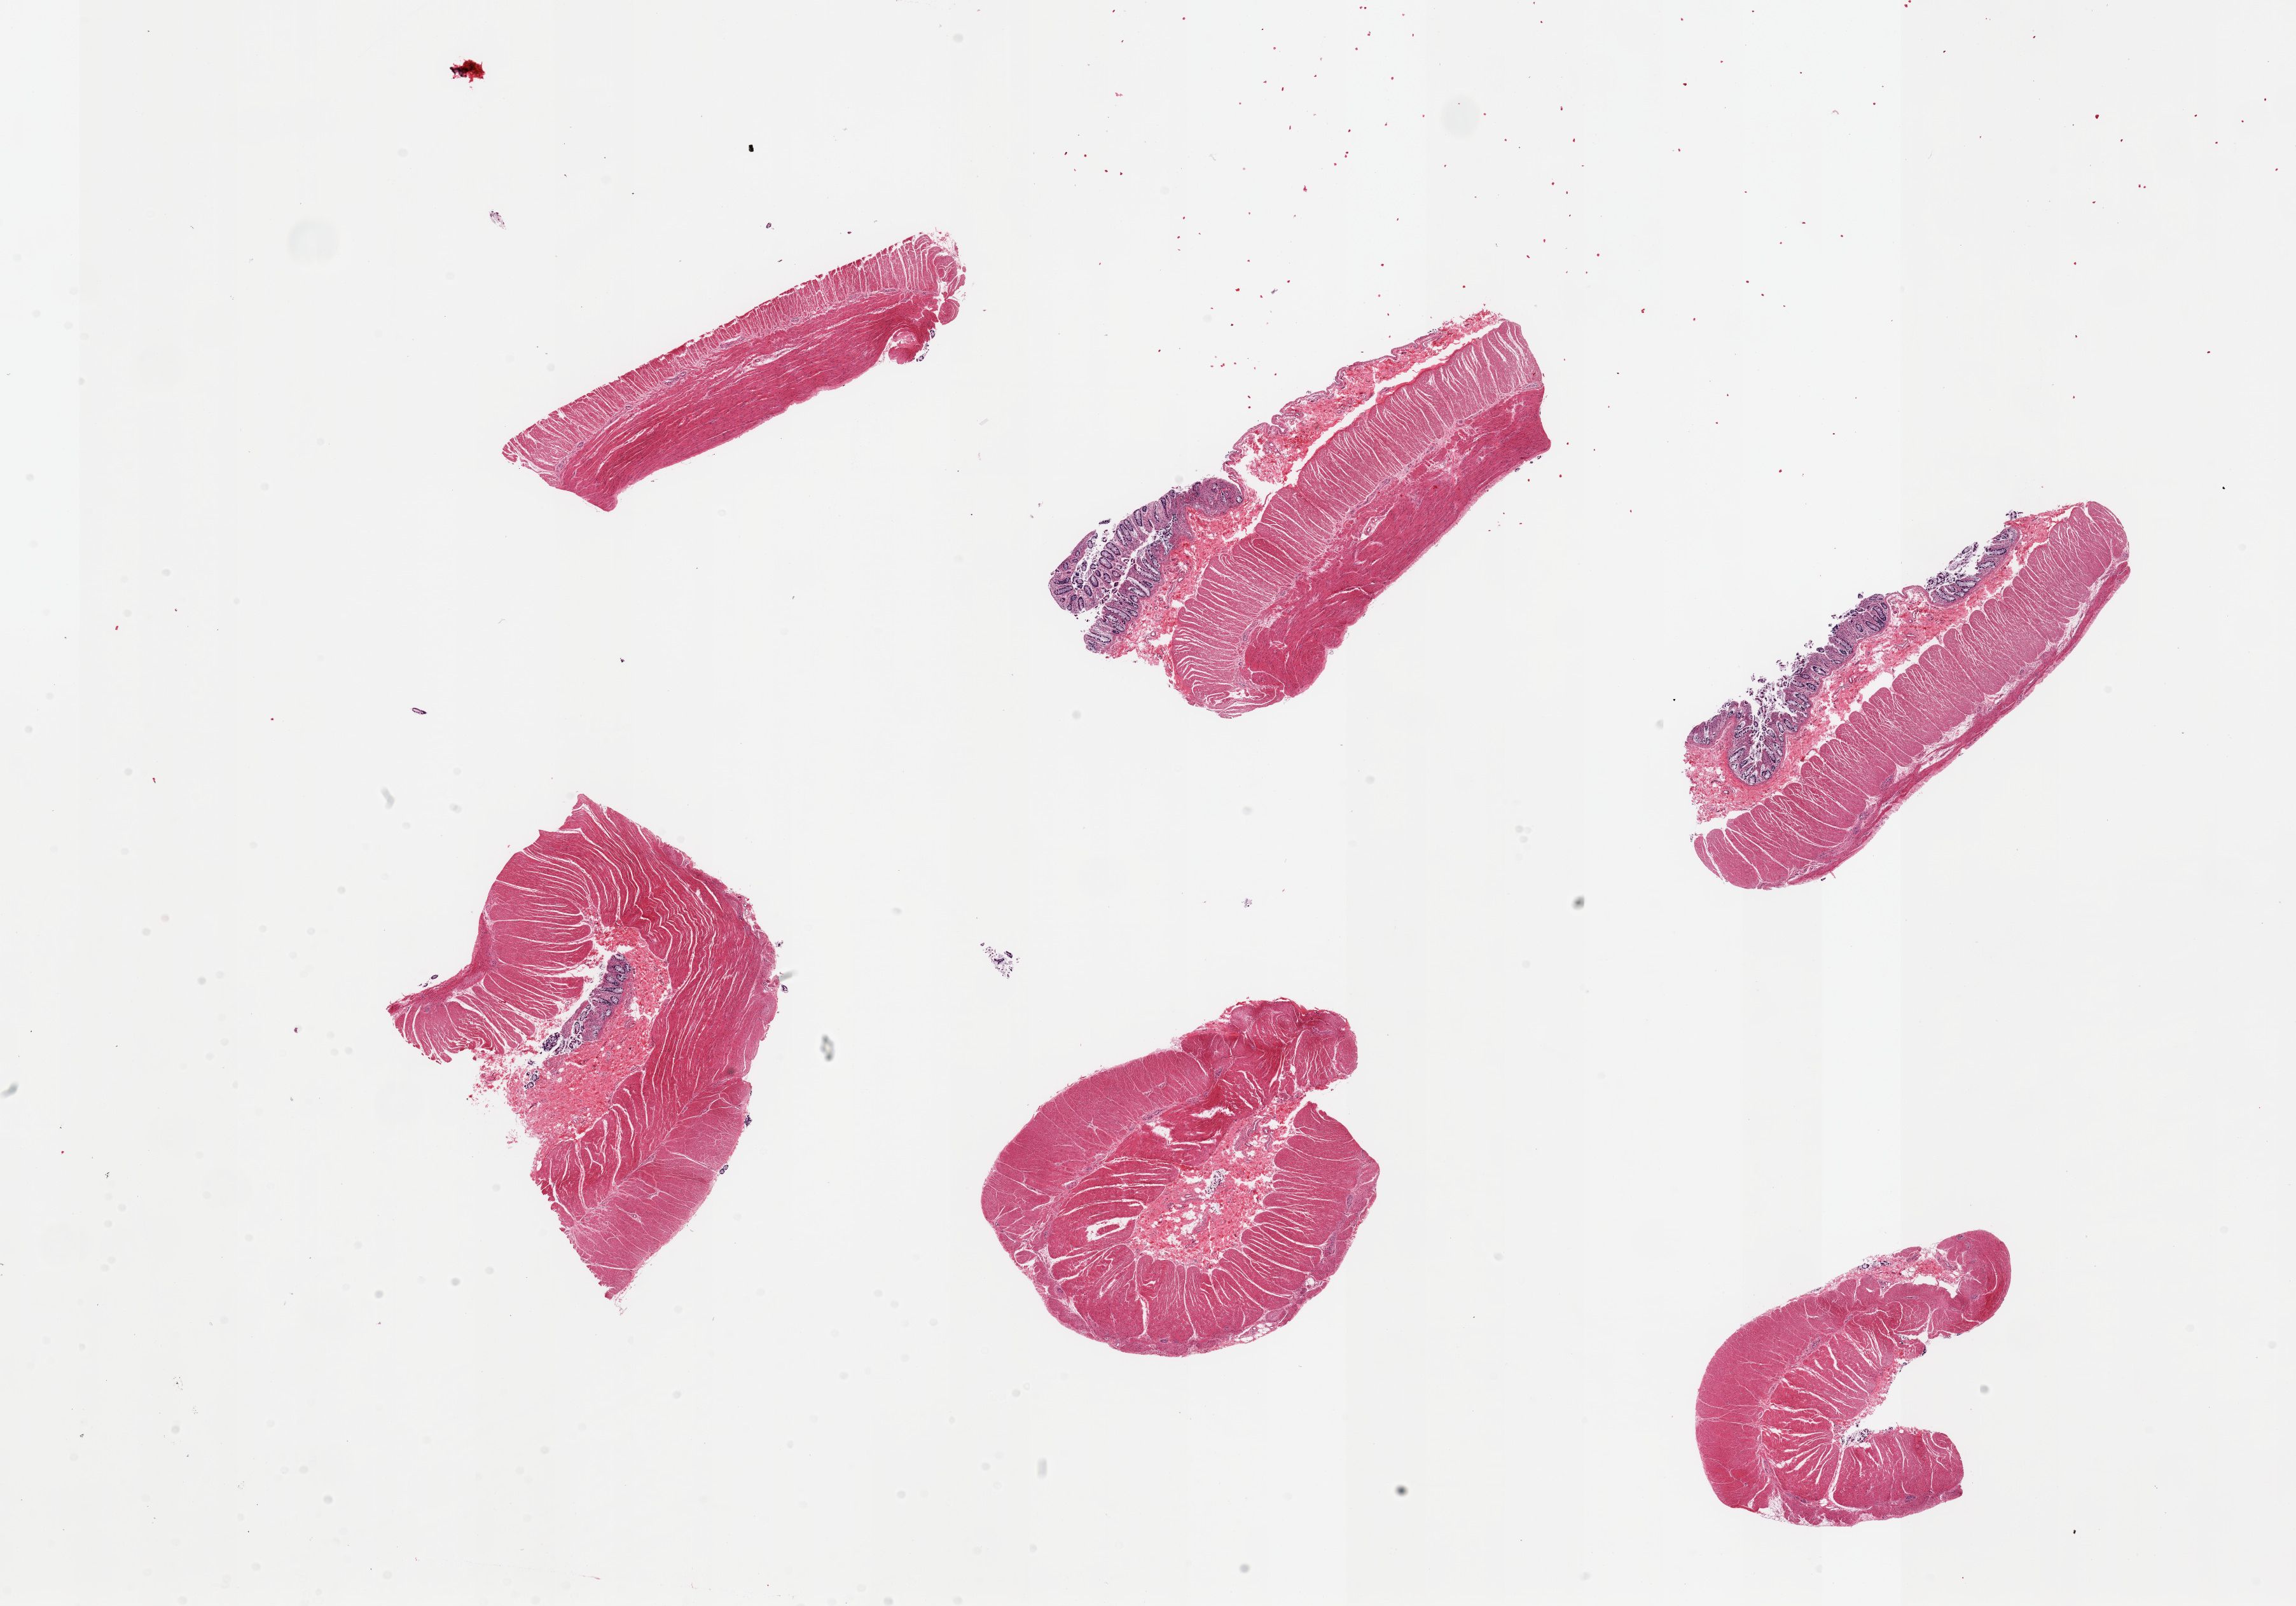
Whole-slide image, H&E stain, shown as a low-resolution overview of the whole scanned area (about 28.5 x 20.0 mm), PAXgene-fixed paraffin-embedded (PFPE) section, target tissue: sigmoid colon, donor tissue sample. Donor sex: male.
- reviewer comment on this tissue sample: 6 pieces, trace autolyzed mucosa, confiremd target muscularis